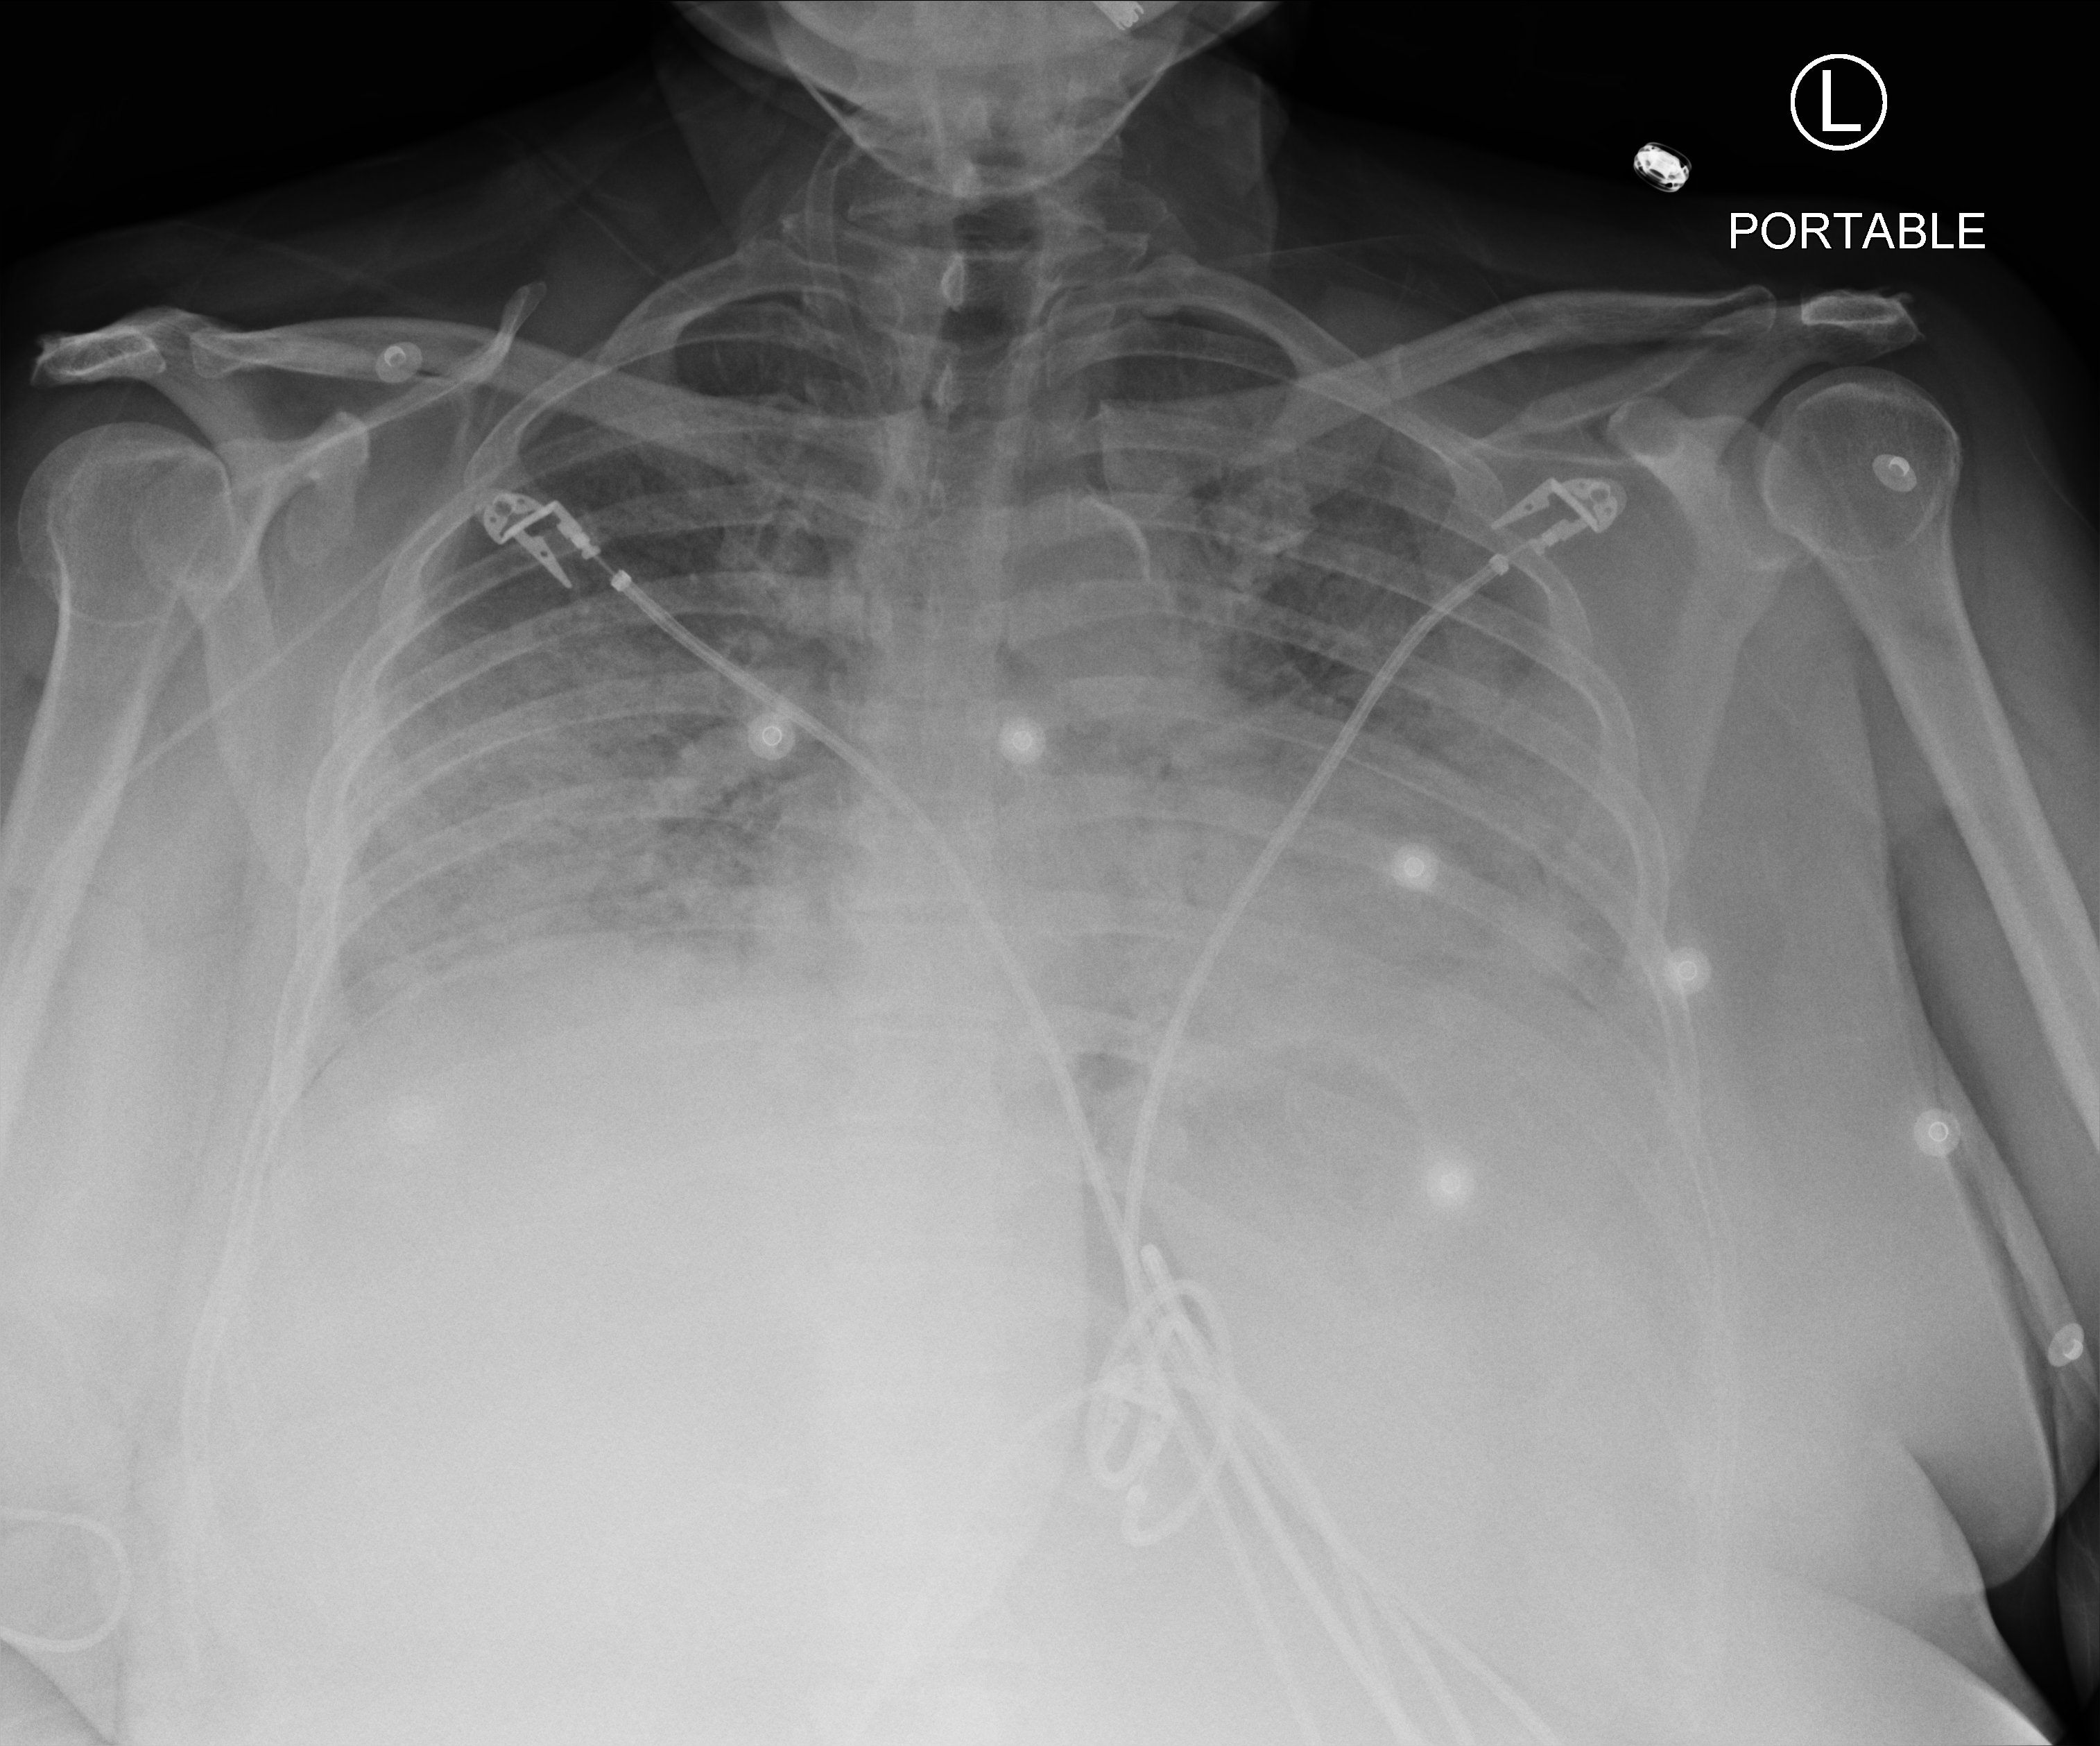
Chest X-ray (portable). Patient hospitalised with COVID-19; female, aged 18–59 years.
Admission-level facts for this patient (not findings on this image; timing relative to this image not recorded):
- hypertension (admission record): yes